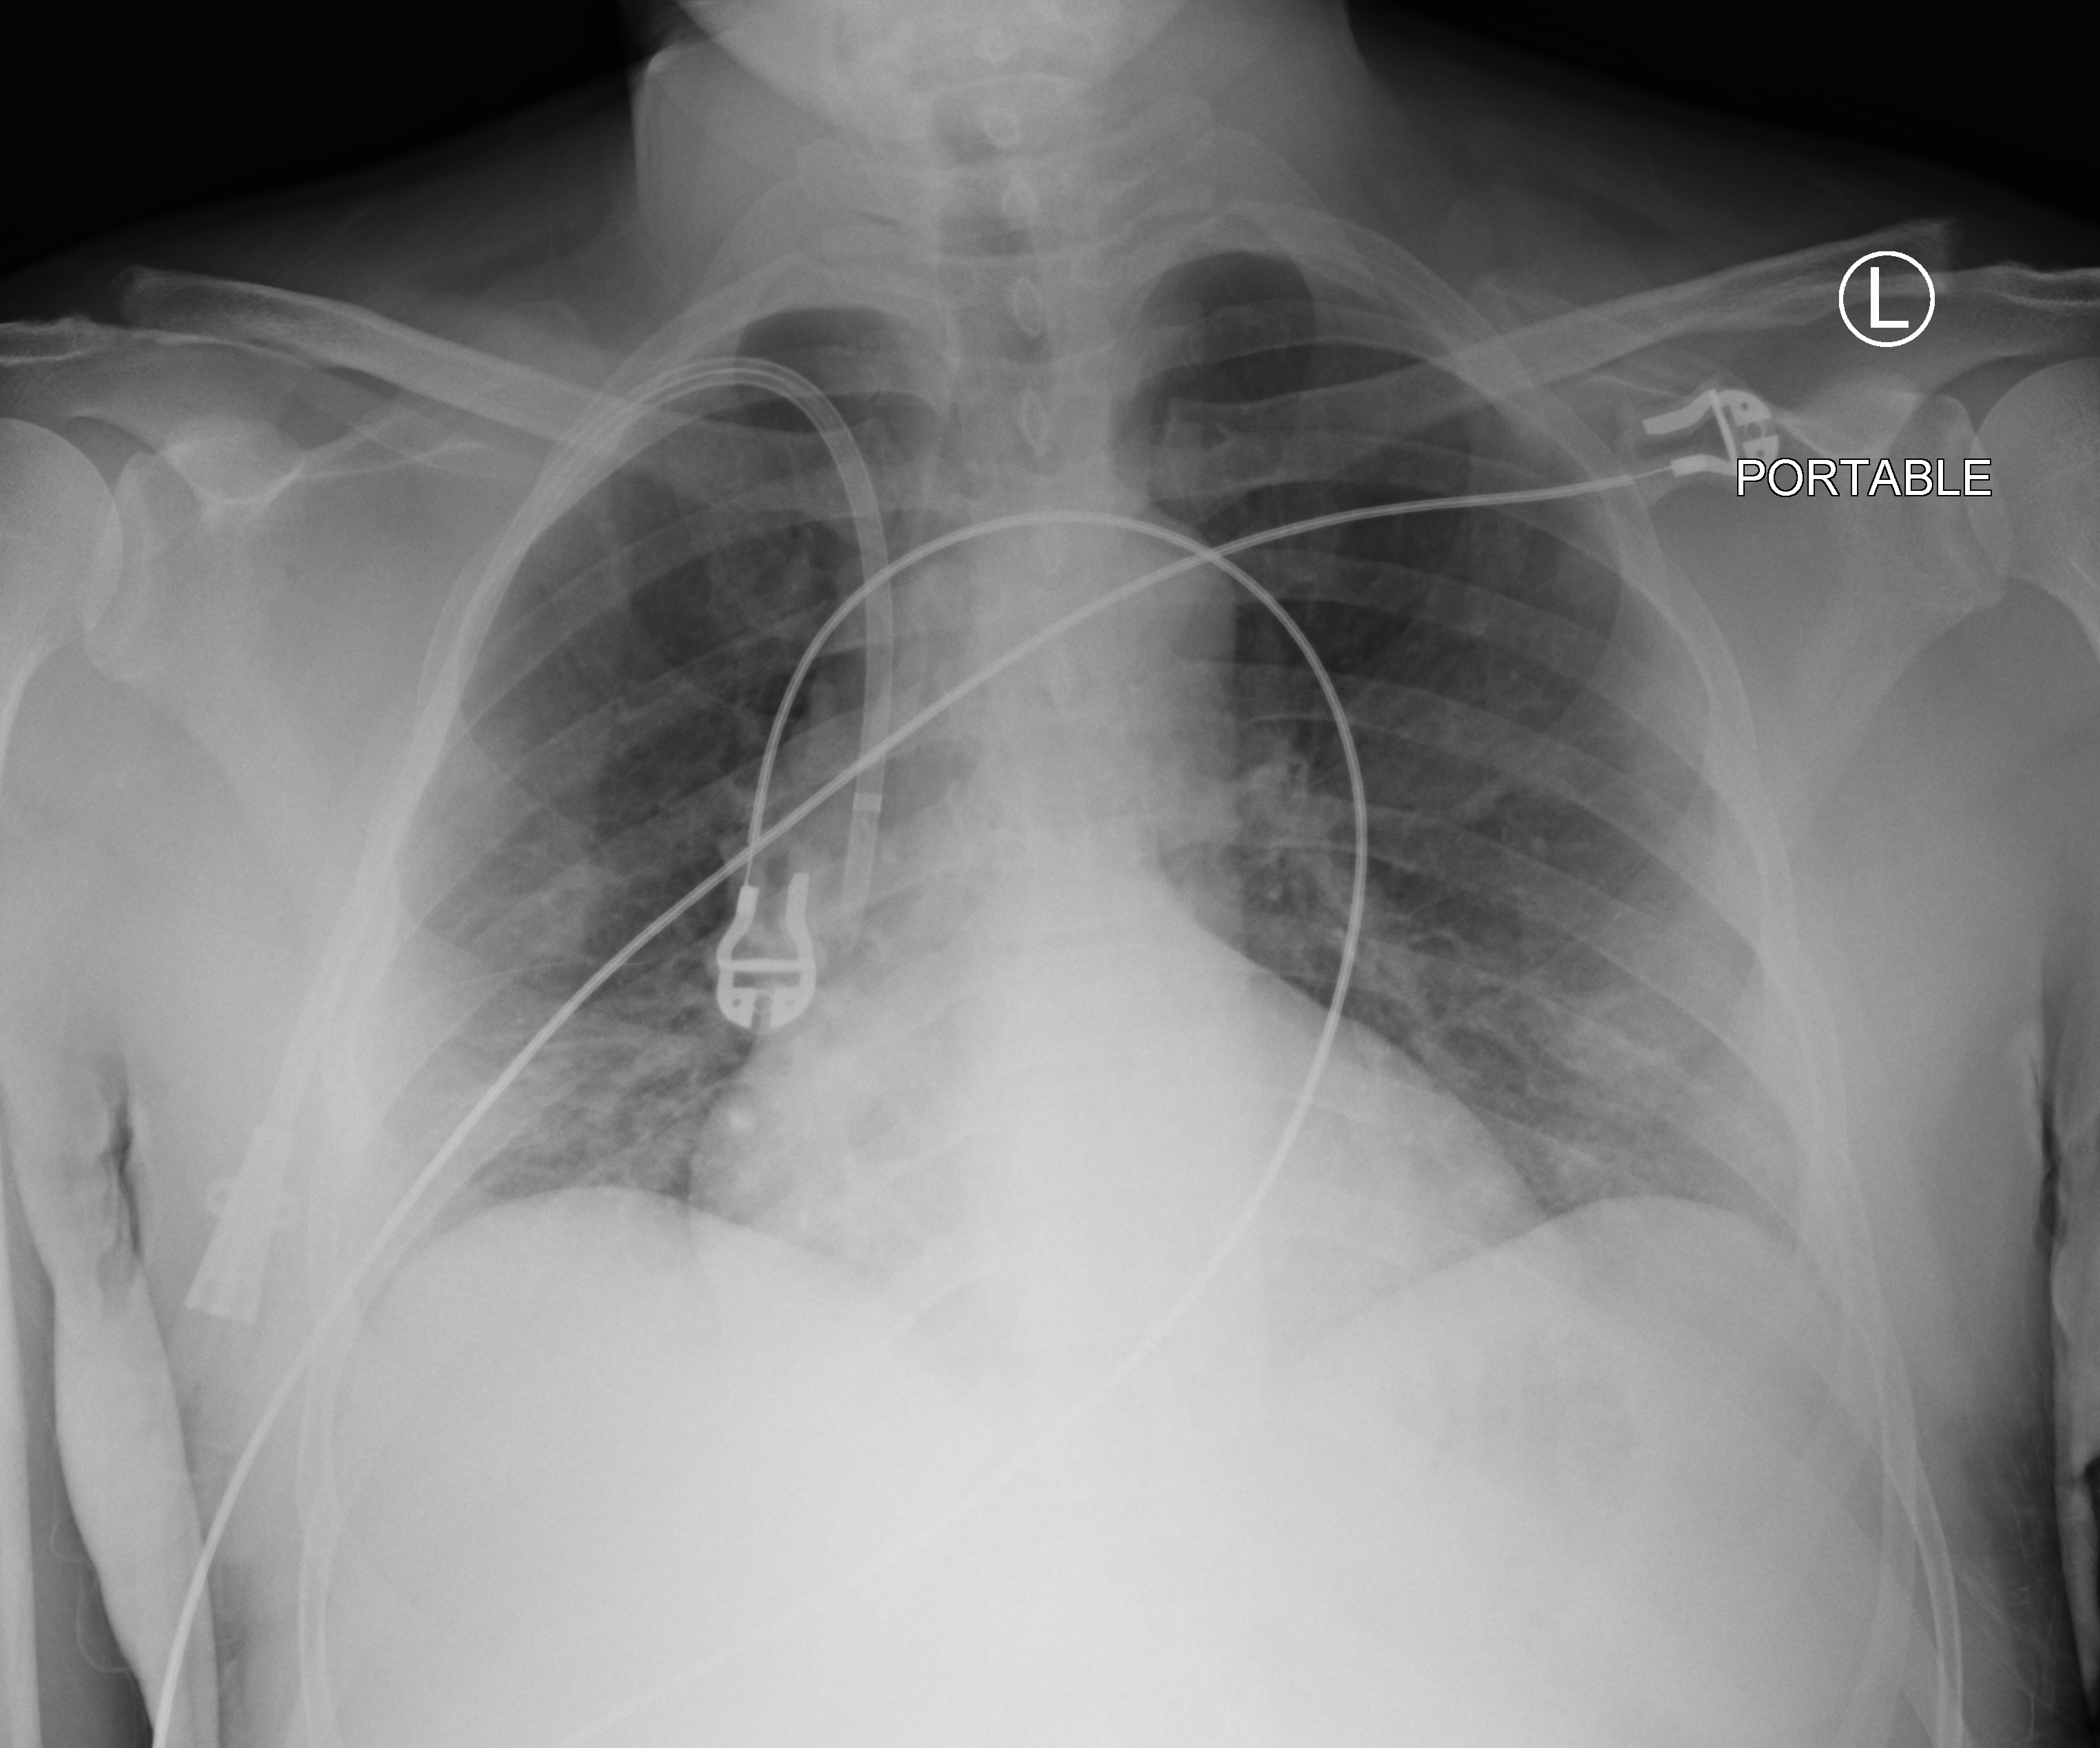
Bedside chest radiograph (computed radiography), anteroposterior (AP) projection. Male patient hospitalised with COVID-19, age 18–59 years.
Admission-level facts for this patient (not findings on this image; timing relative to this image not recorded):
- admitted to intensive care during this hospital stay: no